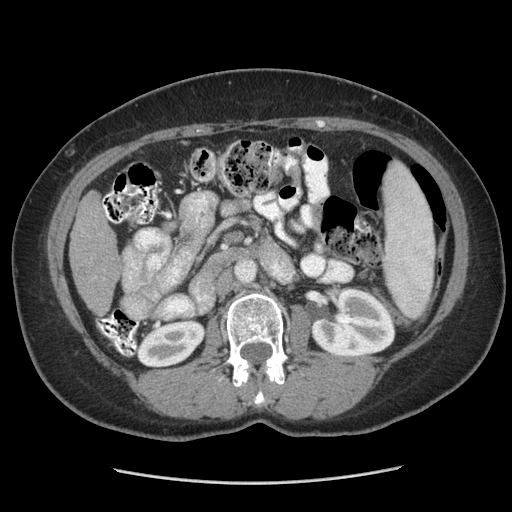
Contrast-enhanced abdominal CT (liver protocol), one axial slice. Slice 121 of 185 in the series (ordered by position). Reconstruction kernel STANDARD. 140 kVp. Soft-tissue window (W 400 / L 40 HU). 2.5 mm slice thickness. 512 × 512 image matrix. Case-level facts recorded for this patient, not image findings: diagnosis: hepatocellular carcinoma (patient treated with transarterial chemoembolisation; whether this scan precedes or follows treatment is not stated here); TNM stage (as recorded): Stage-I; Child-Pugh class: A; tumour differentiation: poorly differentiated; tumour nodularity: uninodular.
Outlined on this slice (semi-automatically segmented with operator editing):
- liver parenchyma outside the tumour (the mass and vessels are separate outlines, so this box may not span the whole liver): bounding box <68,192,118,314> (left, top, right, bottom; pixels)